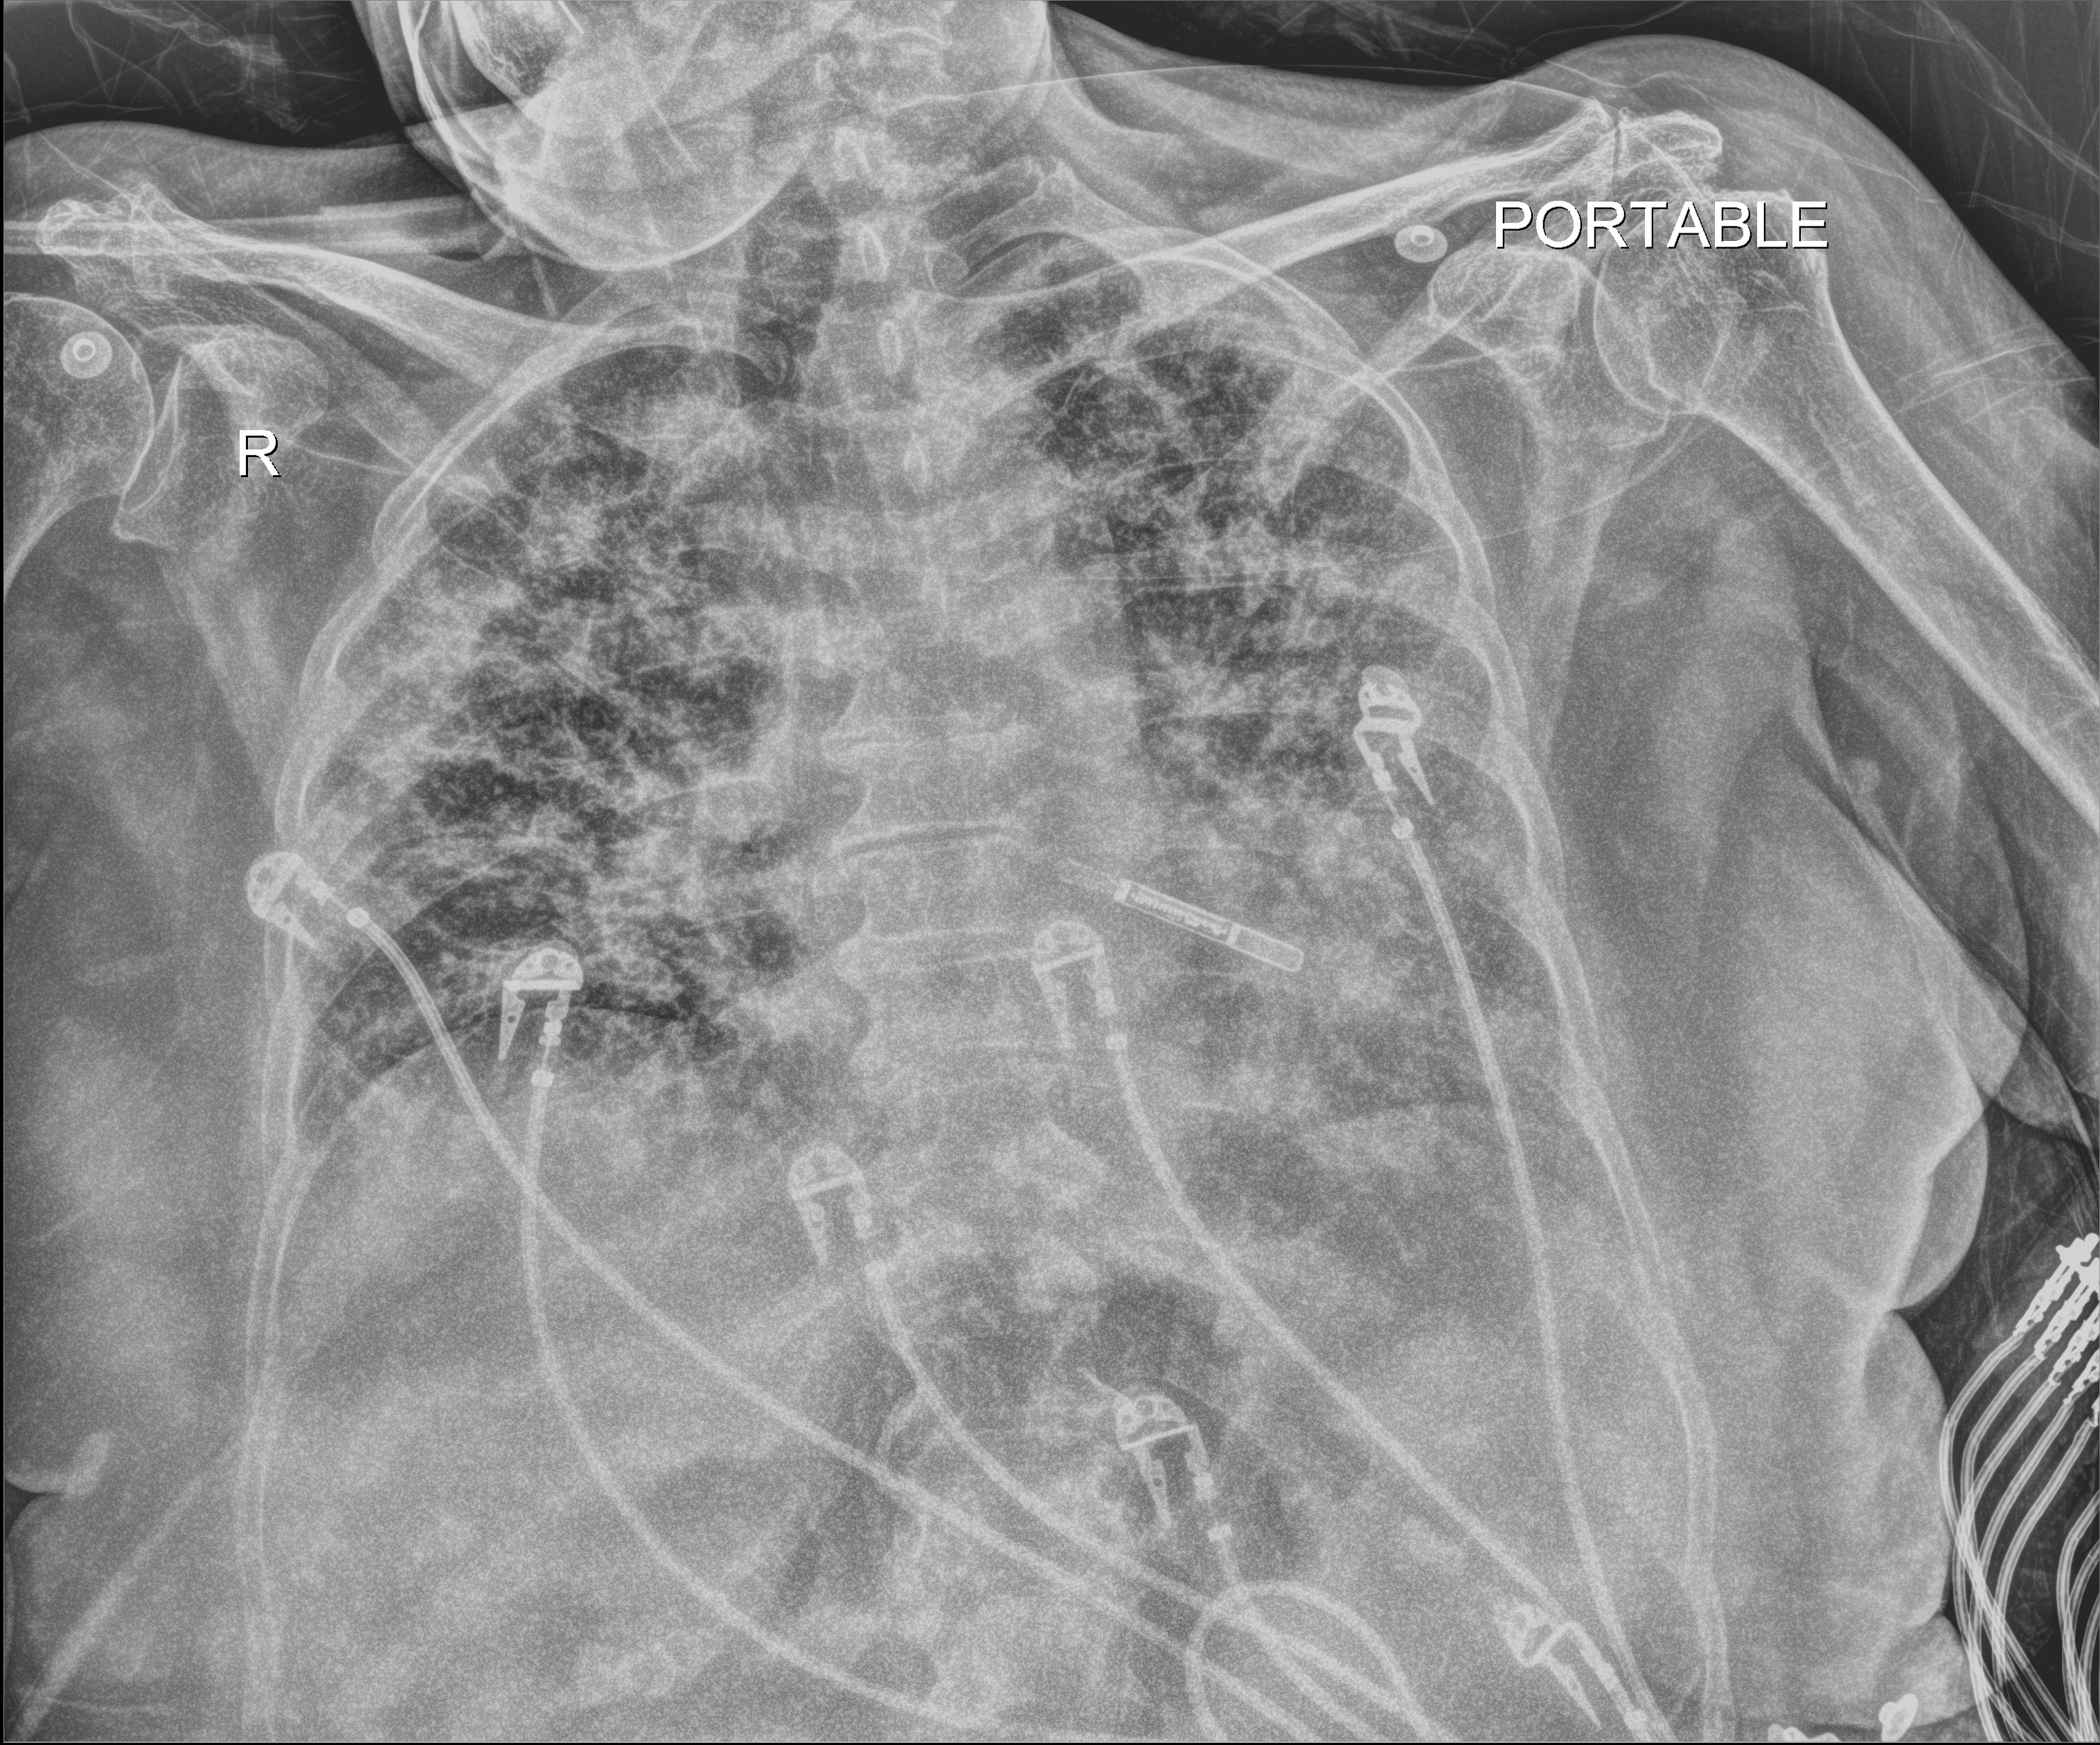
Chest X-ray; anteroposterior (AP) projection. Female patient hospitalised with COVID-19, age 75–90 years.
Hospital-stay facts (about this admission, not read from this image; timing relative to this image not recorded):
- admitted to intensive care during this hospital stay: no
- length of hospital stay: 10 days